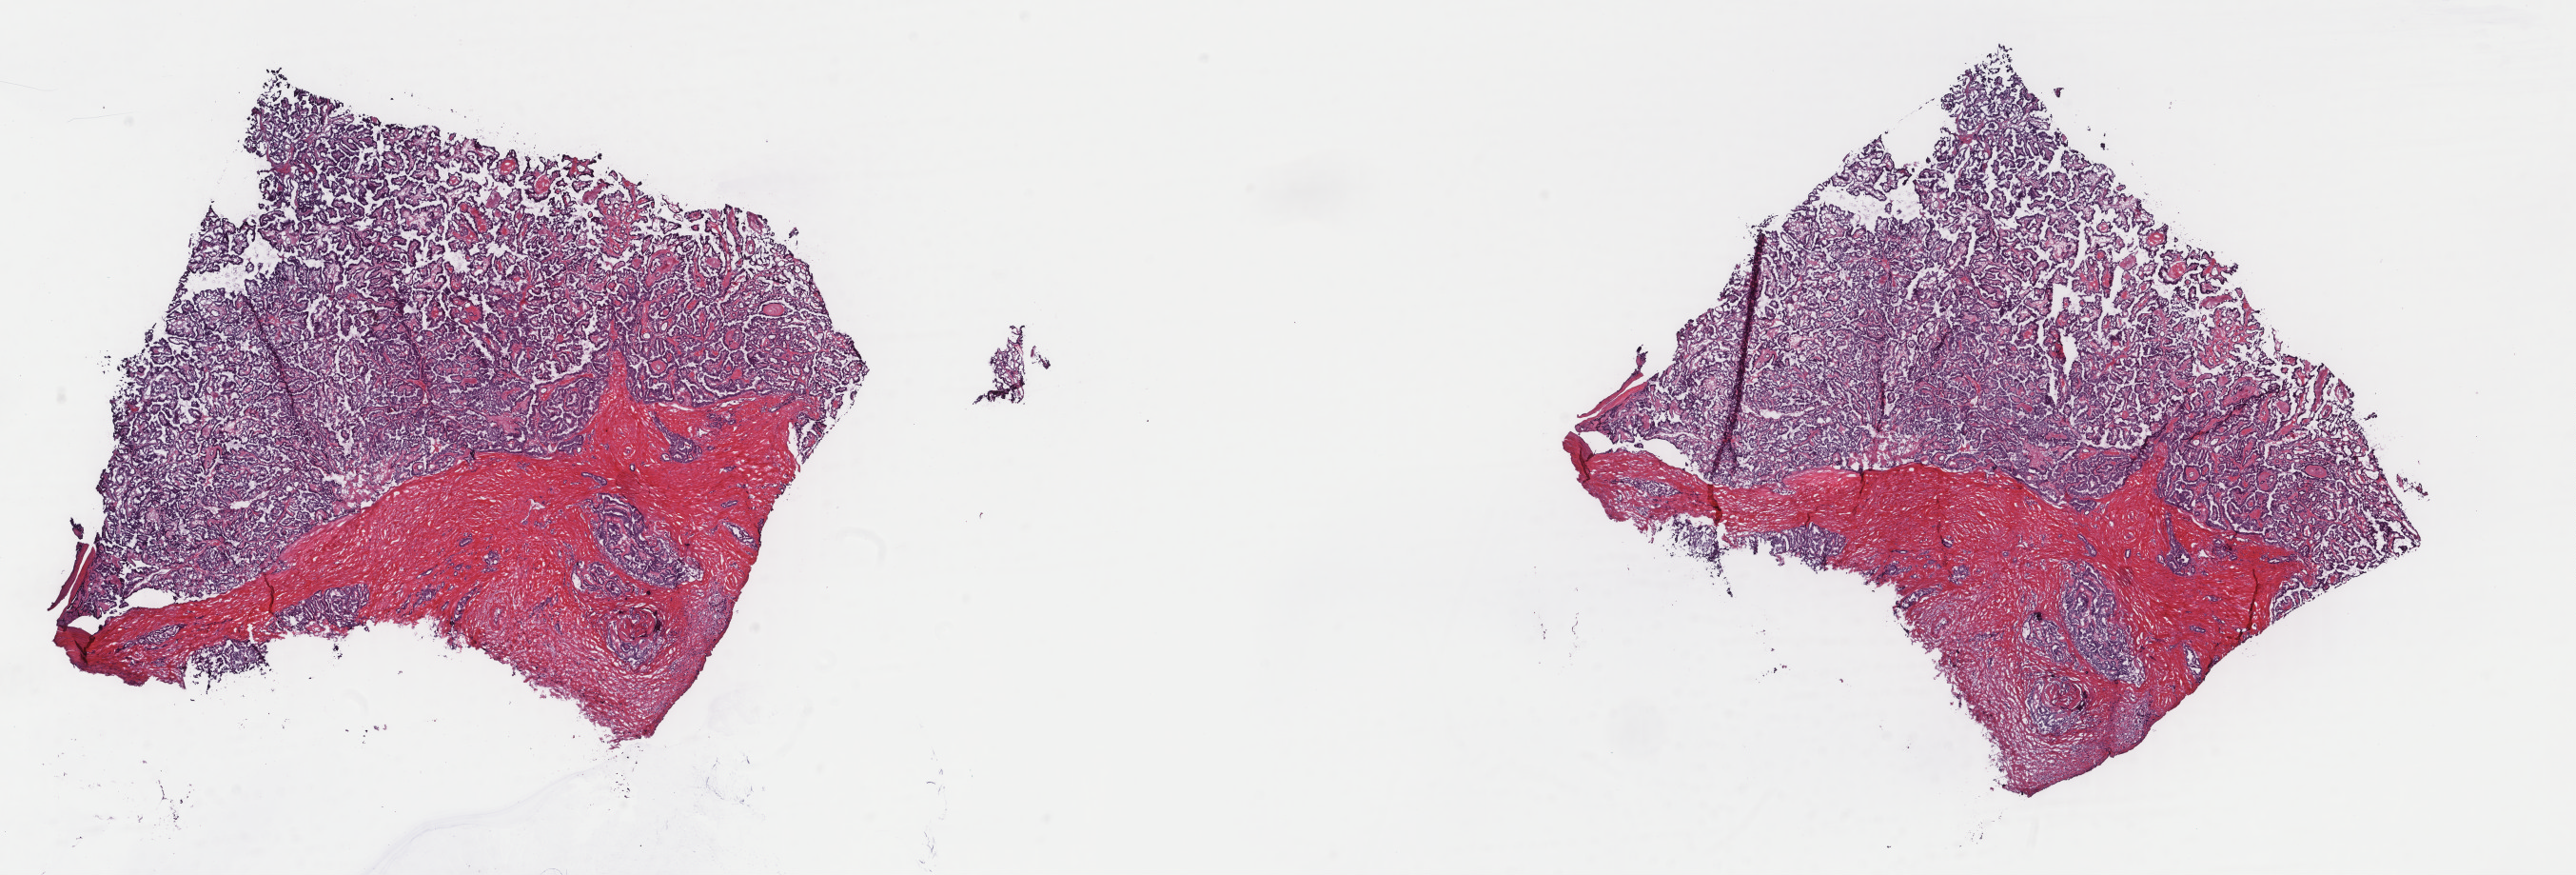
Whole-slide histology image, Hematoxylin and eosin (H&E) stained, low-resolution overview of the scanned area, about 21.5 x 7.3 mm; frozen section from the top of the tissue portion; thyroid, primary tumour sample. Male patient; age at initial diagnosis 39 years. Slide review estimates, as recorded: tumour cells 60%, tumour nuclei 100%, normal cells 0%, stromal cells 40%, necrosis 0%. Inflammatory infiltration, as recorded: lymphocyte infiltration 0%, monocyte infiltration 1%, neutrophil infiltration 0%.
Lymph nodes positive (case pathology): 23 of 106 examined. AJCC pathologic stage: I (7th edition). Diagnosis: Papillary adenocarcinoma, NOS (thyroid gland).